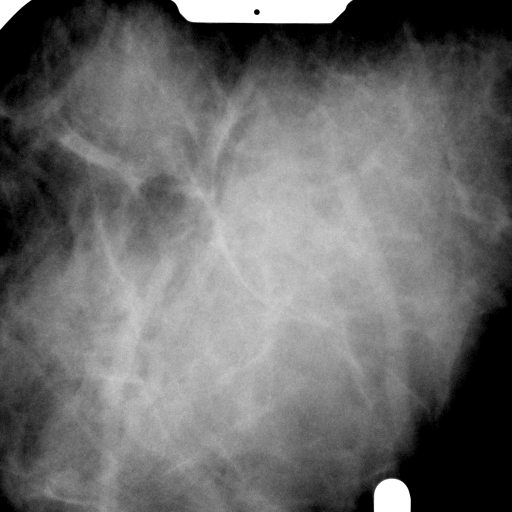
Spot-compression mammographic view.
Pathology recorded for this patient (not read from this image): pathology diagnosis: benign fibroadenoma (right breast); pathology report notes: RIGHT BREAST CALCIFICATION WITH NEEDLE LOCATION: FIBROADENOMA (1.9CM). REMAINING BREAST TISSUE WITH ADENOSIS, FOCAL FIBROADENOMATOUS CHANGES, APOCRINE METAPLASIA, FIBROCYSTIC CHANGES, SMALL INTRADUCTAL PAPILLOMAS, AND USUAL TYPE DUCTAL HYPERPLASIA. MICROCALCIFICATIONS ASSOCIATED WITH BENIGN BREAST TISSUE ARE IDENTIFIED. NO IN-SITU OR INVASIVE CARCINOMA.